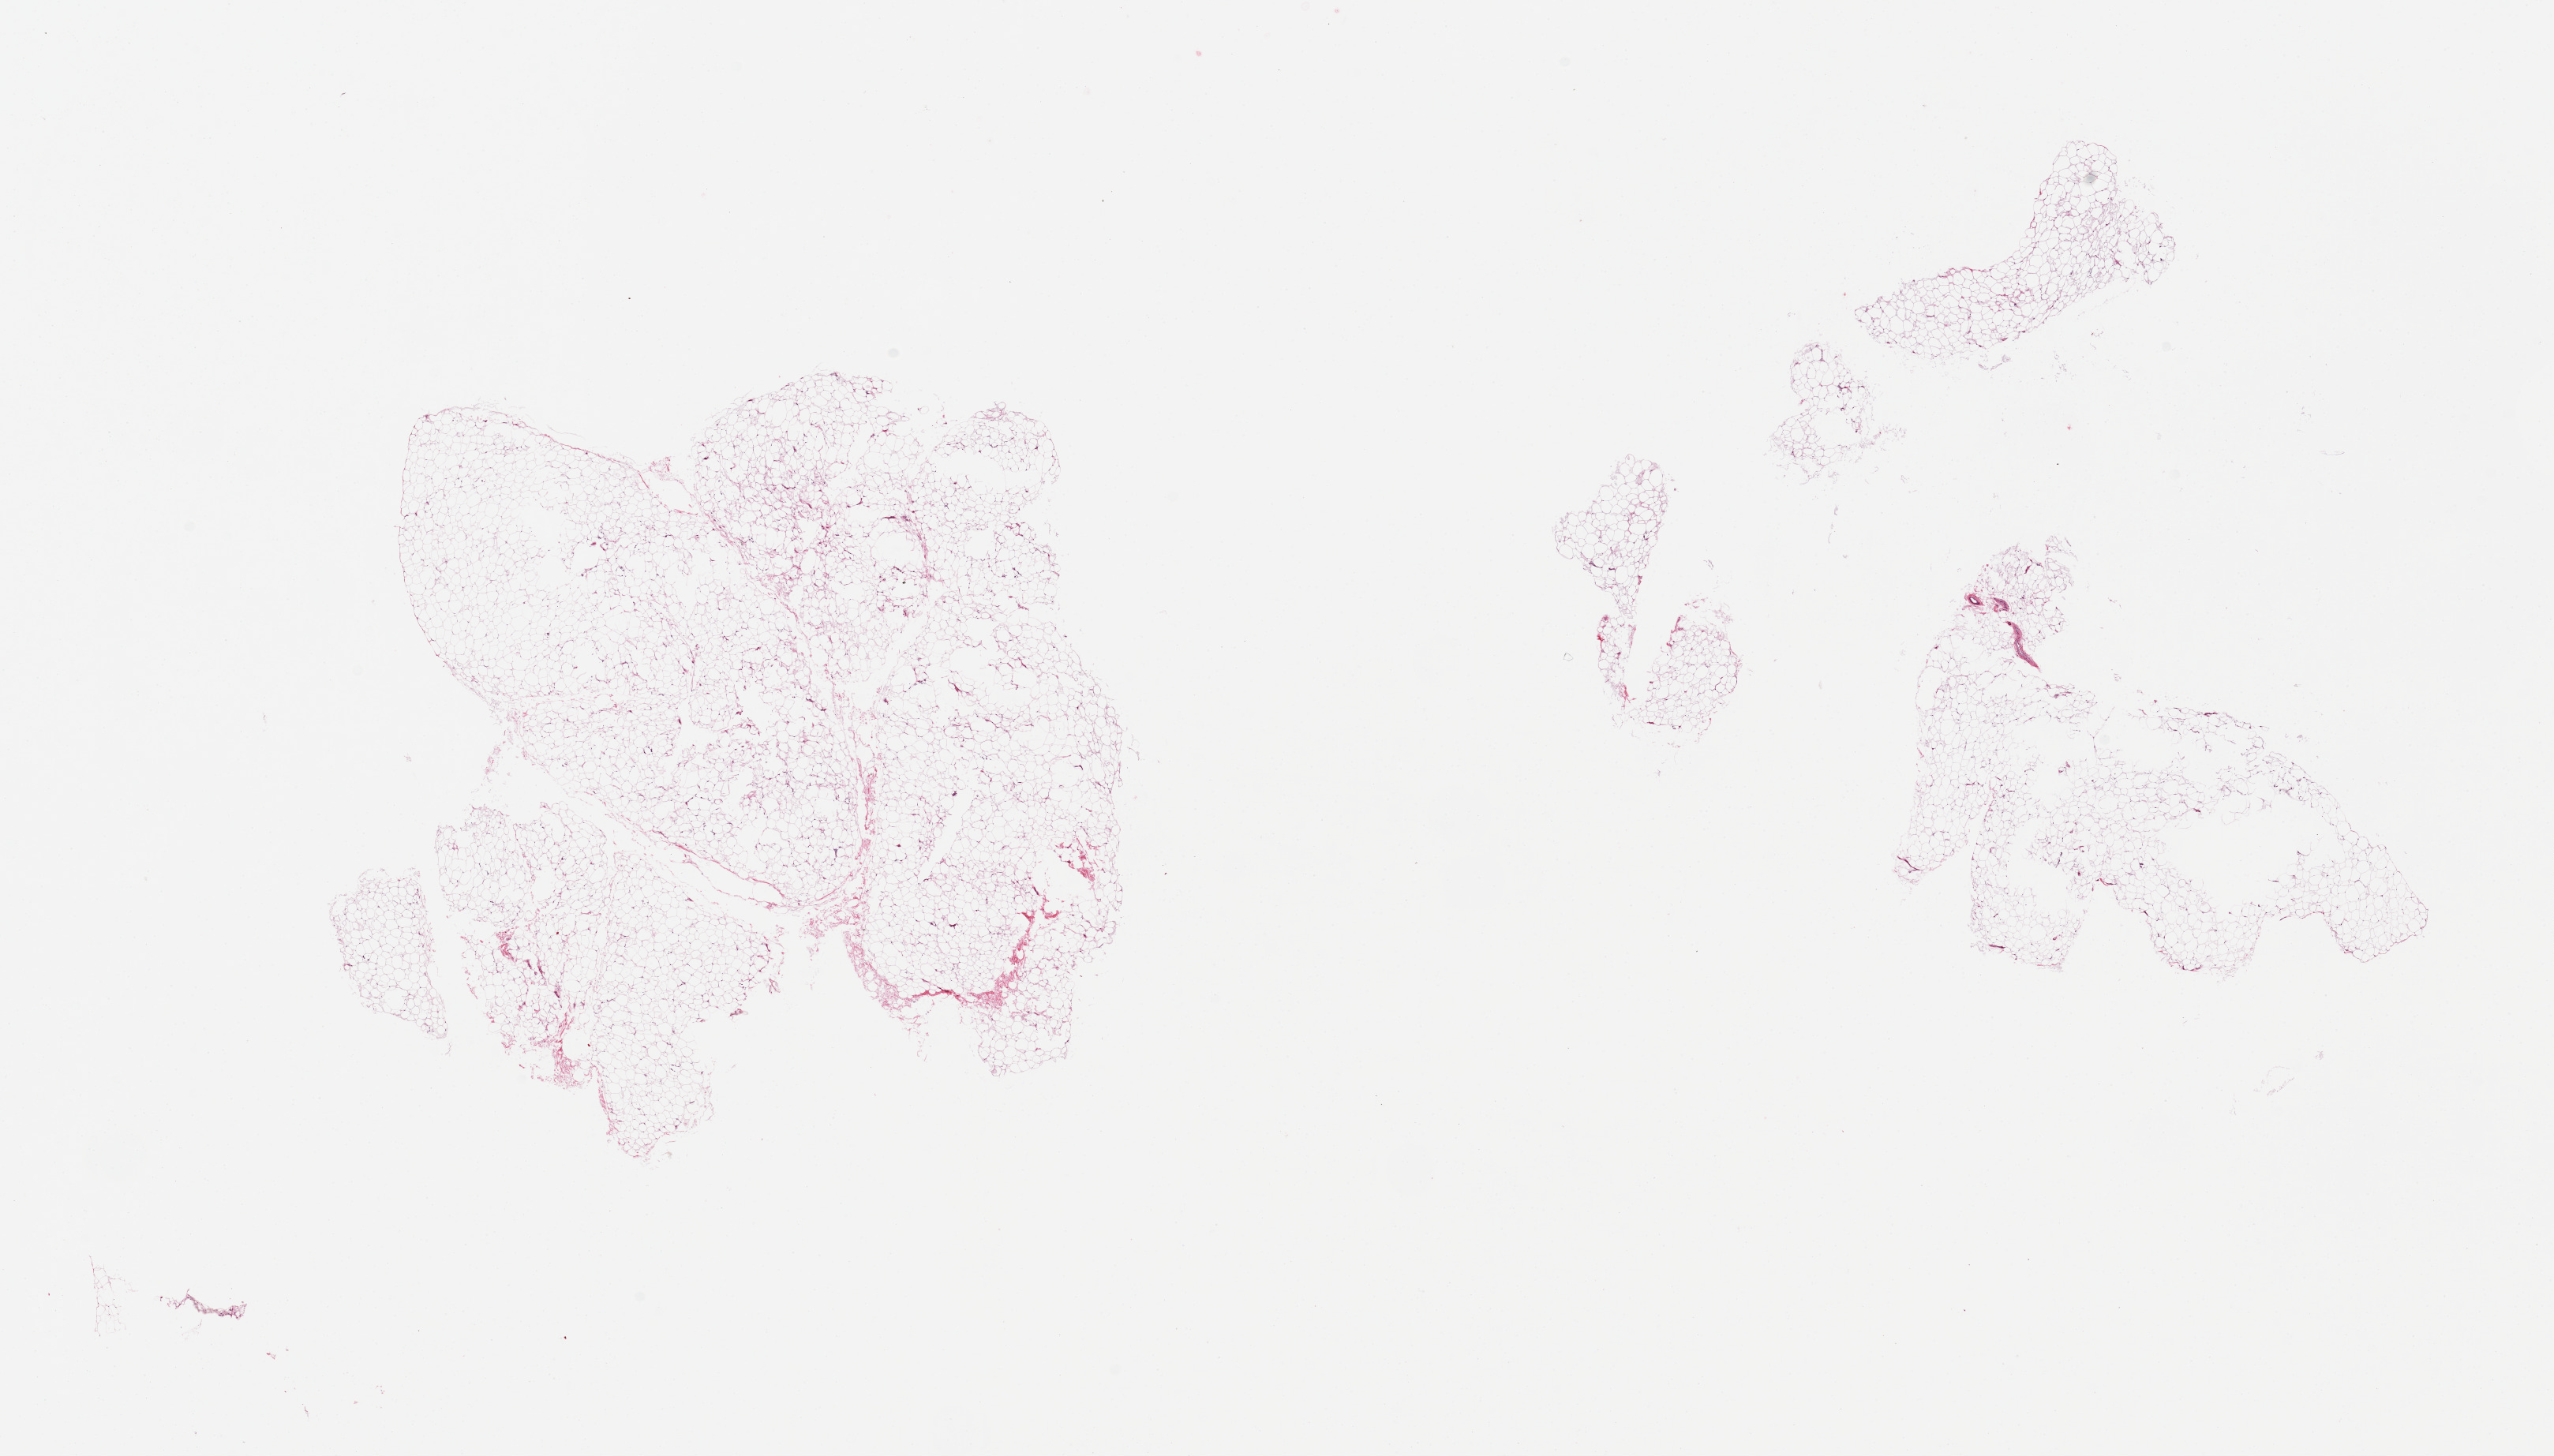
Haematoxylin and eosin whole-slide image, low-resolution overview of the scanned area, about 25.6 x 14.6 mm (slide scanned at 20x). PAXgene-fixed paraffin-embedded (PFPE) section. Section of adipose tissue (target tissue). Tissue donor sample. Donor sex: female.
- pathologist's review note for this sample: 2 fragmented pieces